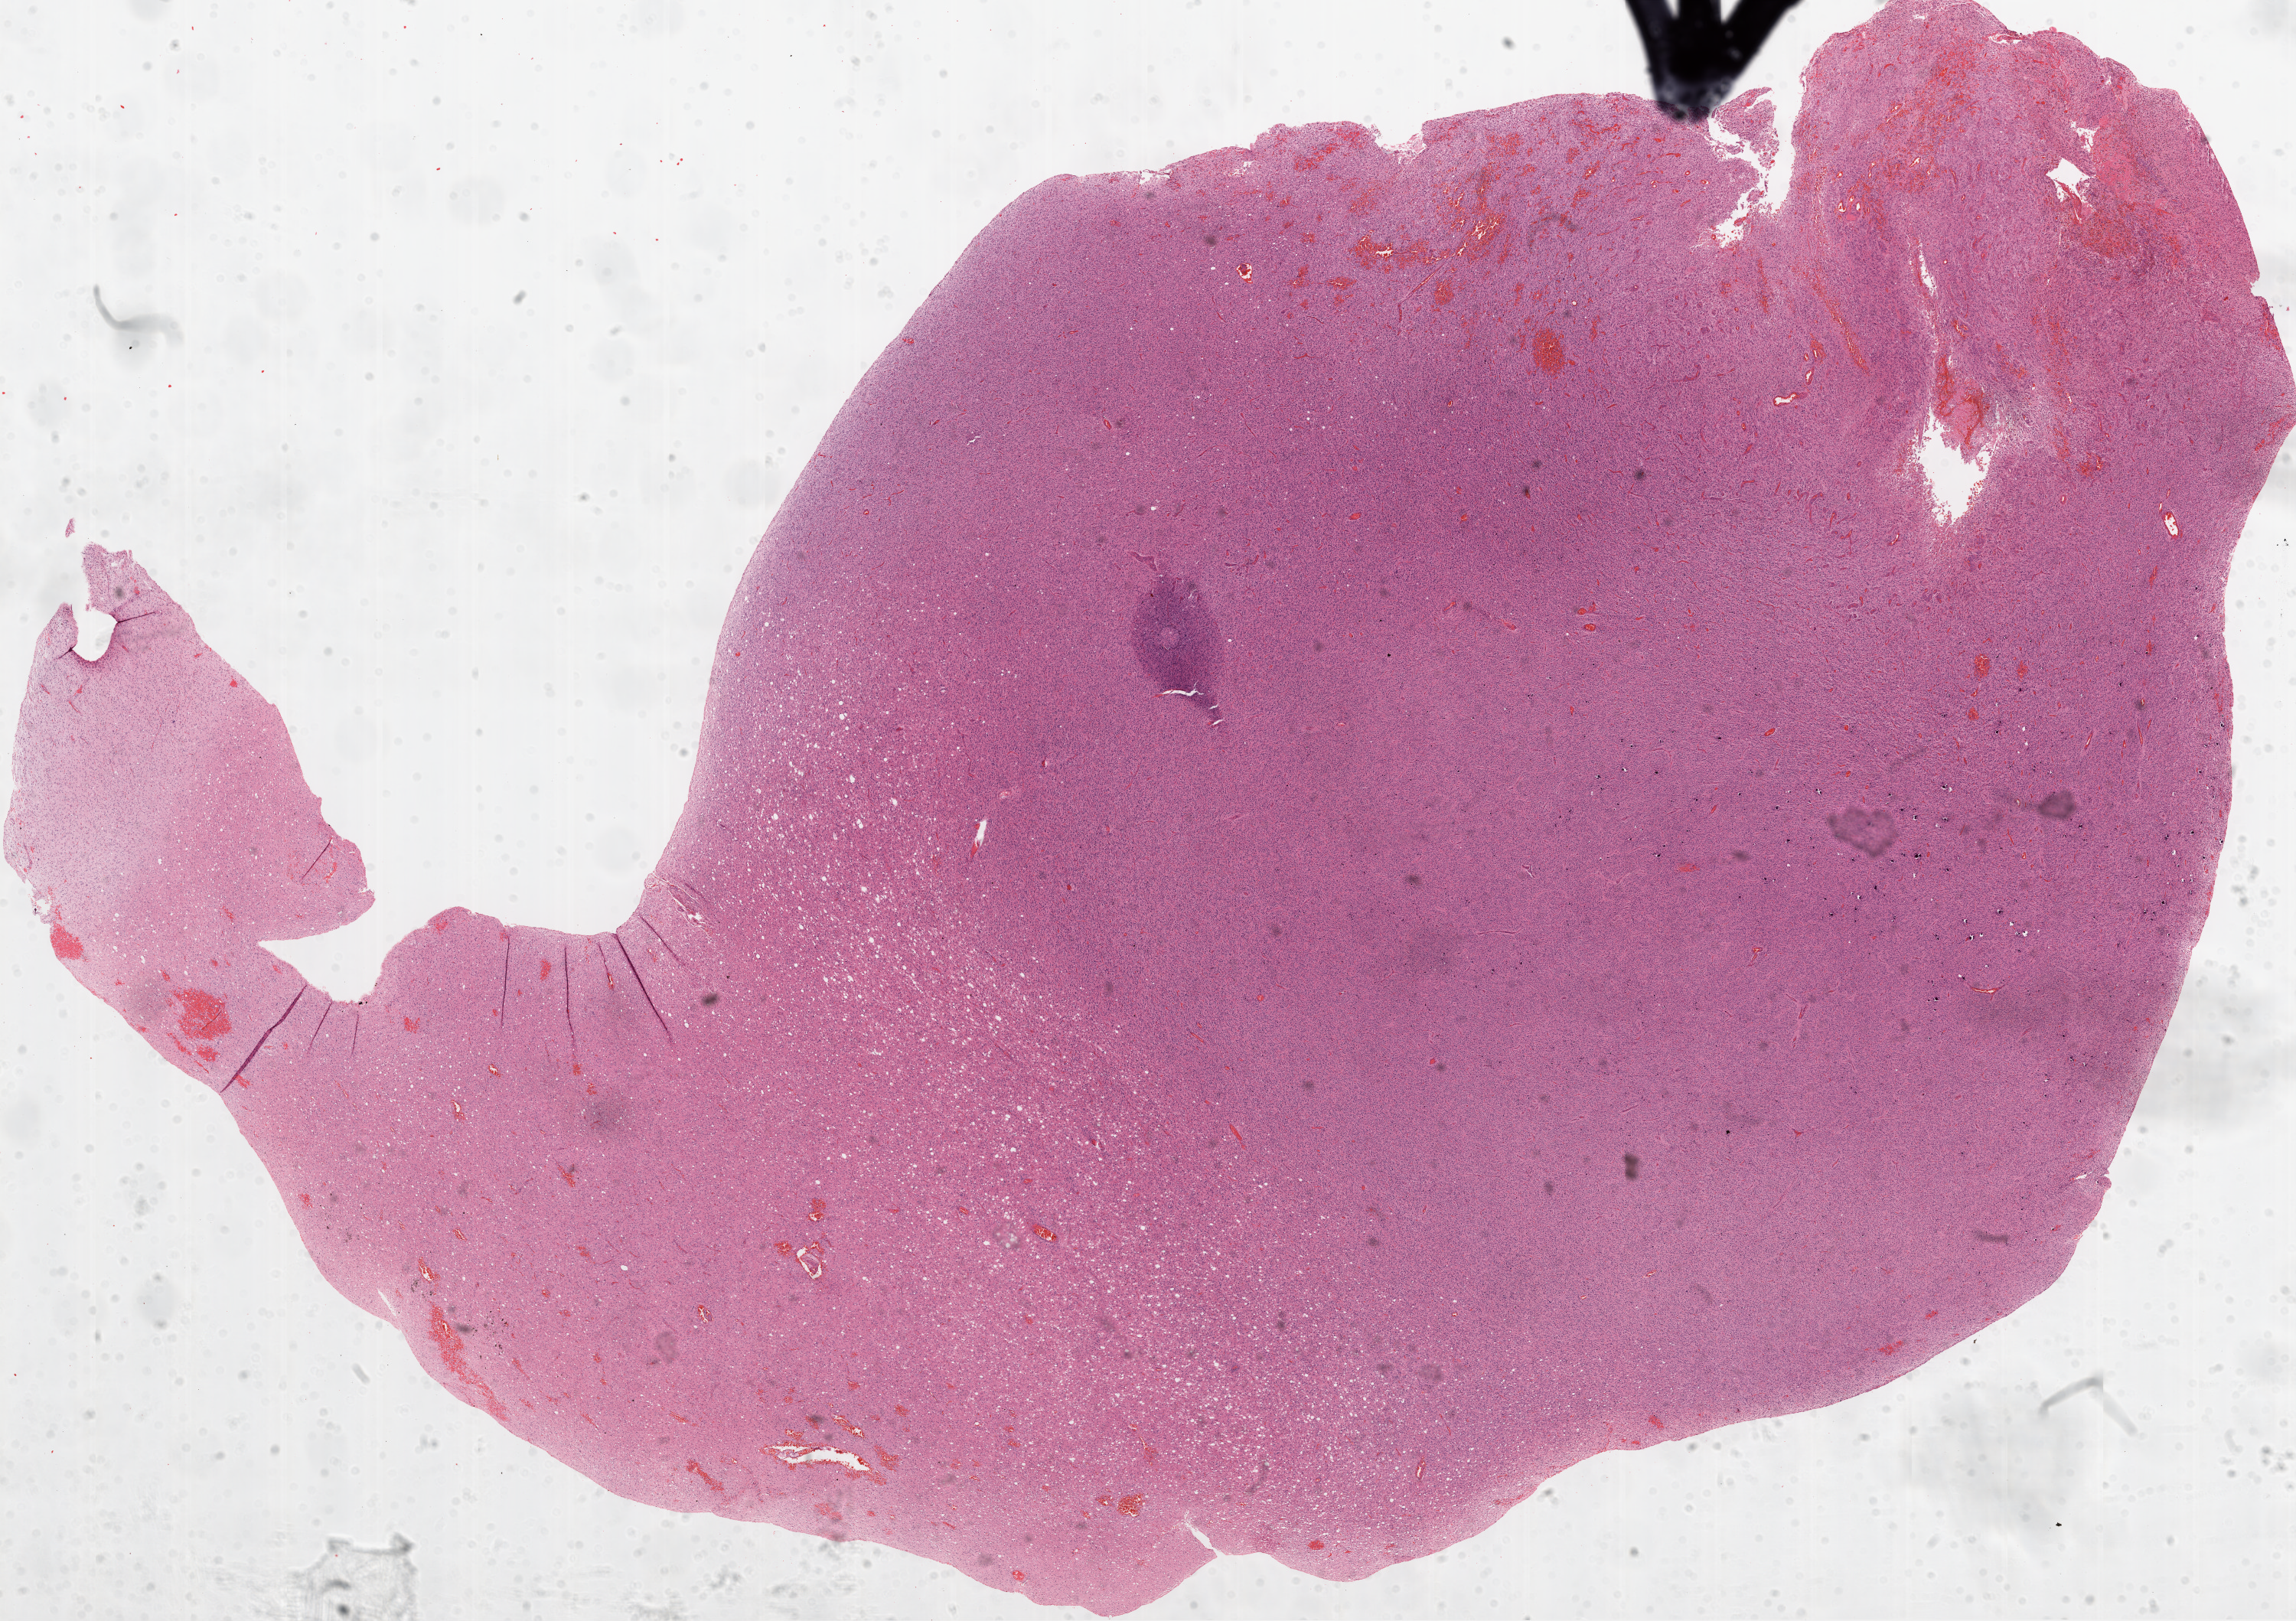
H&E whole-slide image, low-resolution overview of the scanned area, about 24.1 x 17.0 mm (acquisition: 20x scan), formalin-fixed paraffin-embedded (FFPE) diagnostic section, primary tumour sample from the brain. Male patient; age at initial diagnosis 50 years.
- diagnosis: Glioblastoma